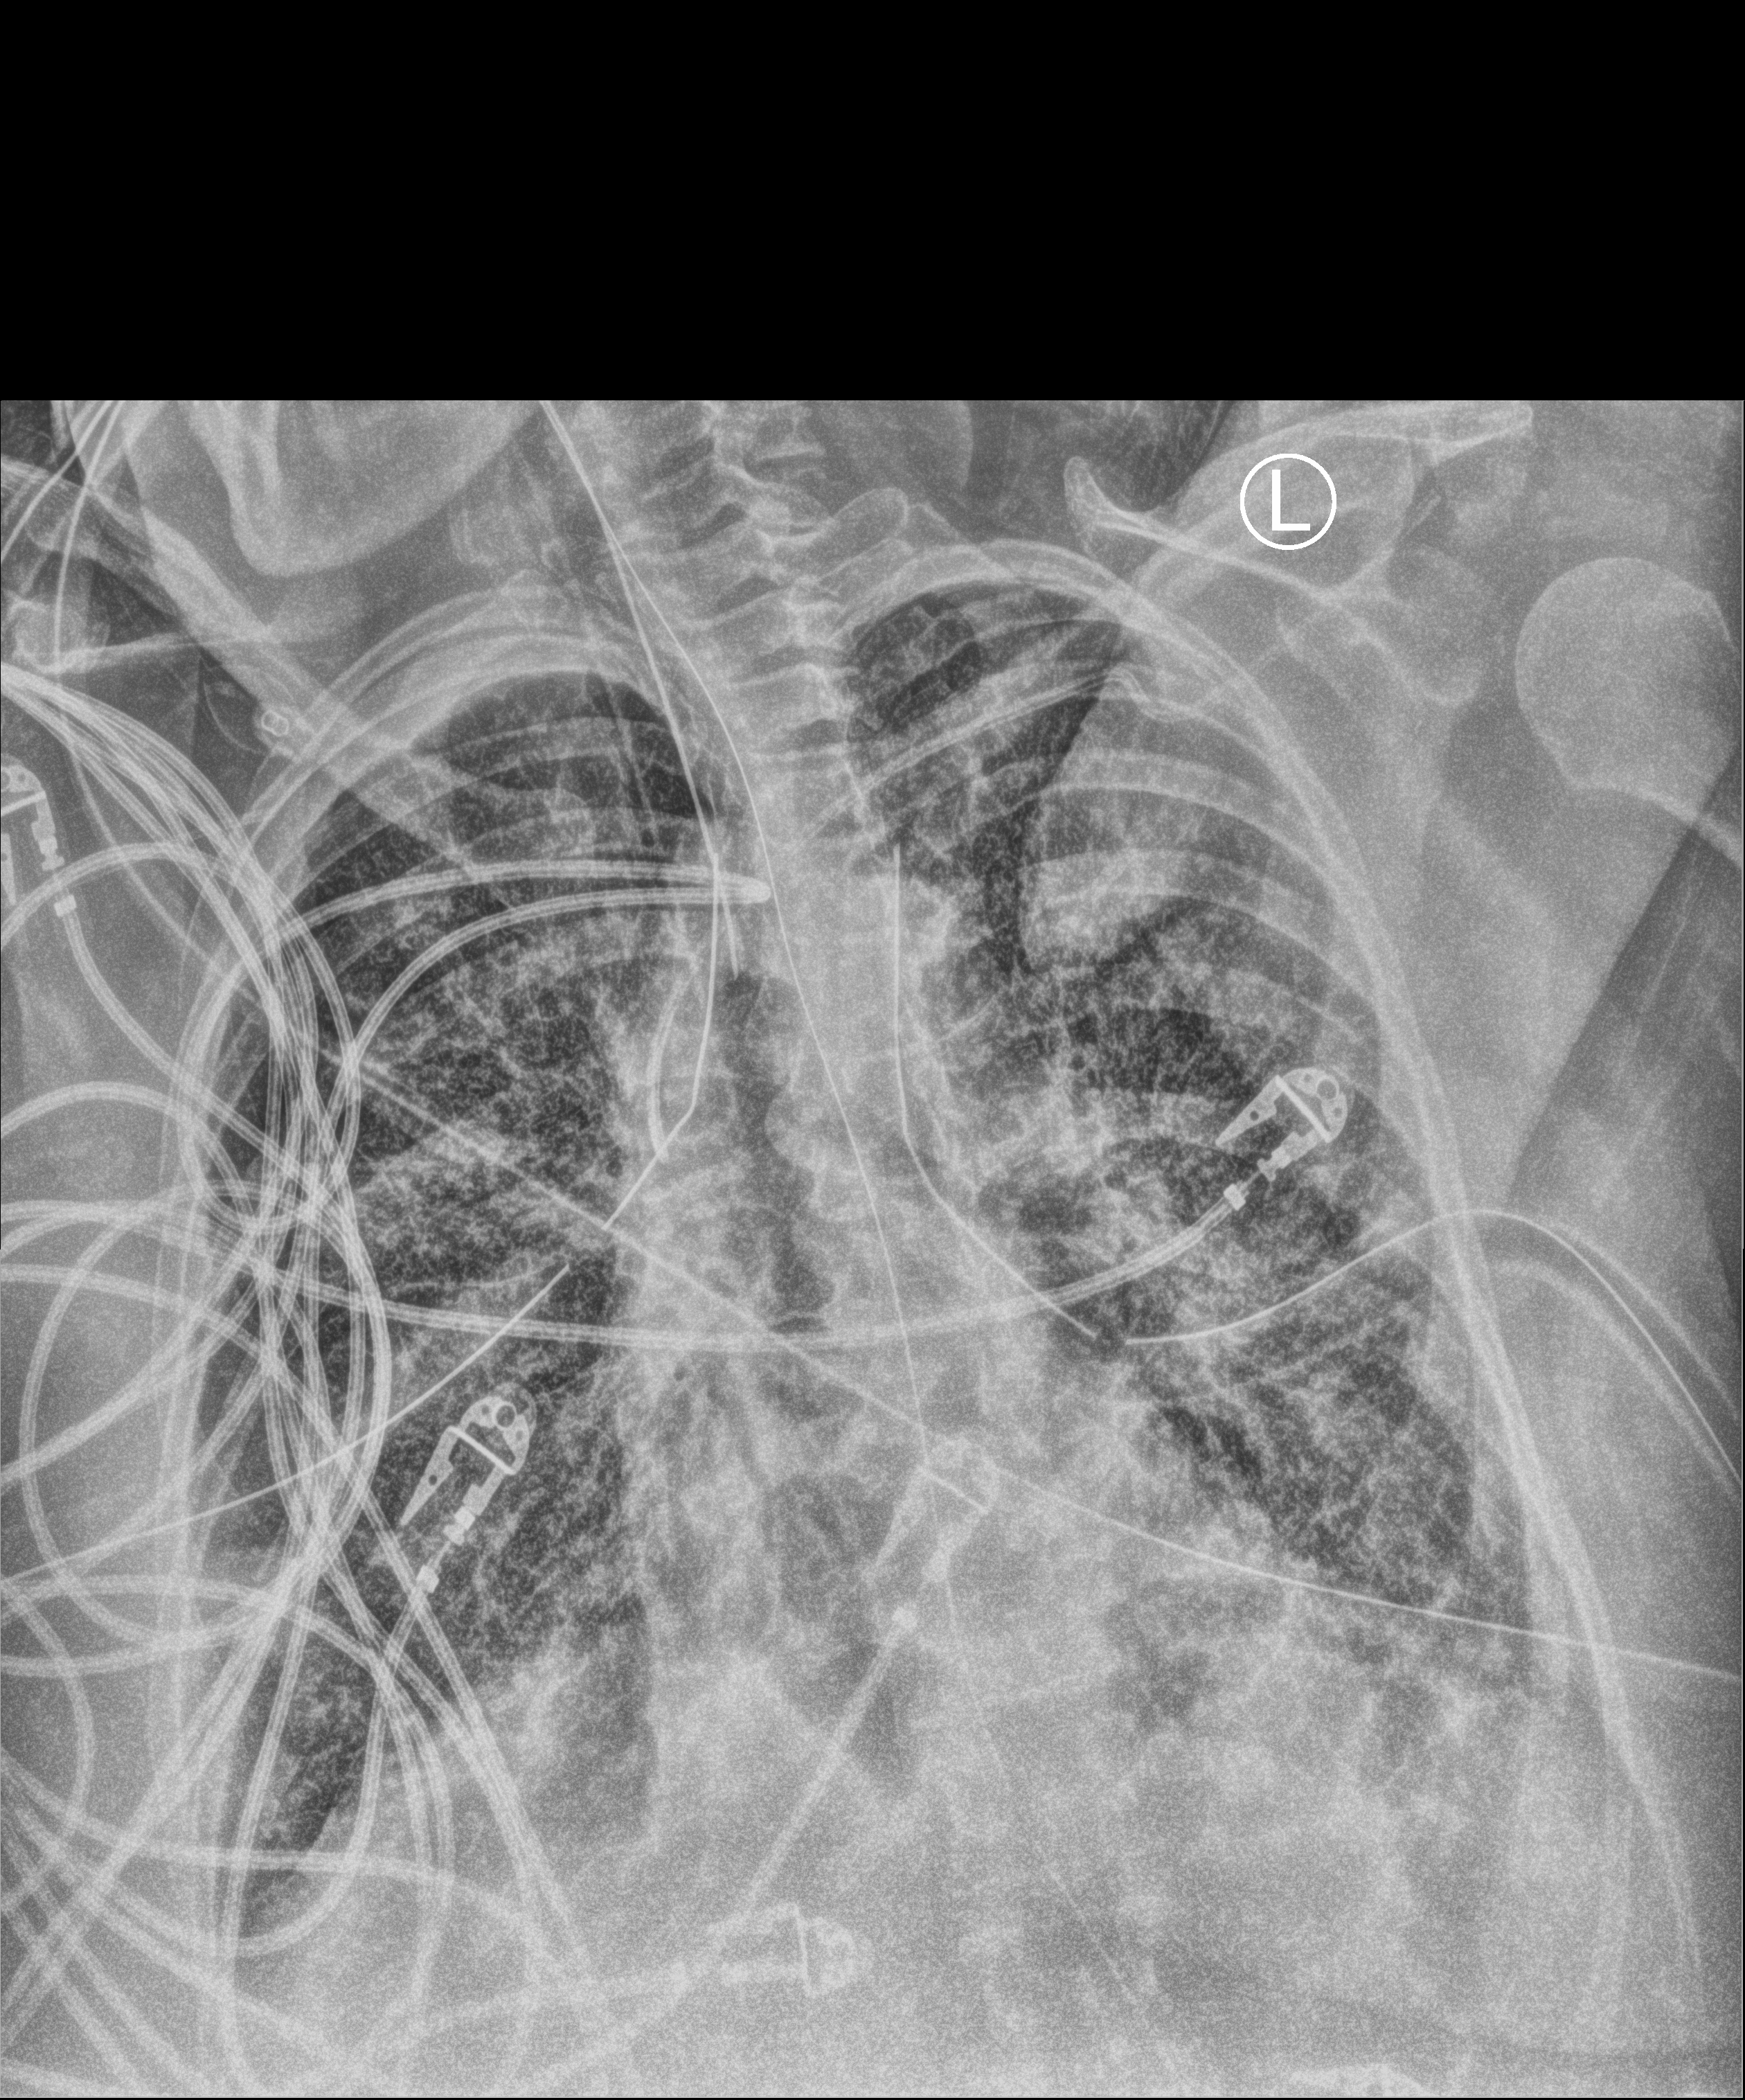
Bedside chest radiograph (computed radiography), anteroposterior (AP) projection. Female patient hospitalised with COVID-19, age 60–74 years.
From the hospital-stay record, not from the radiograph (when in the stay this image was taken is not recorded): admitted to intensive care during this hospital stay: yes.